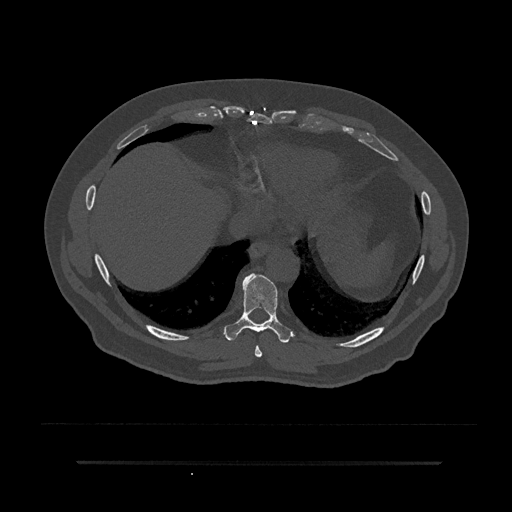
CT including the spine, one axial slice; position 382 of 797 along the scan axis; 120 kVp; bone window (W 1800 / L 400 HU); 512 × 512 image matrix, field of view 464 × 464 mm. Male patient, age 59 years. Case-level facts recorded for this patient, not image findings: primary cancer: bile ducts; vertebrae with lytic lesions (as recorded): T10.
Outlined on this slice (semi-automatically segmented with operator editing):
- T8 vertebra: bounding box (x1, y1, x2, y2) in pixels: (255, 345, 262, 358)
- T9 vertebra: (224, 273, 293, 343)